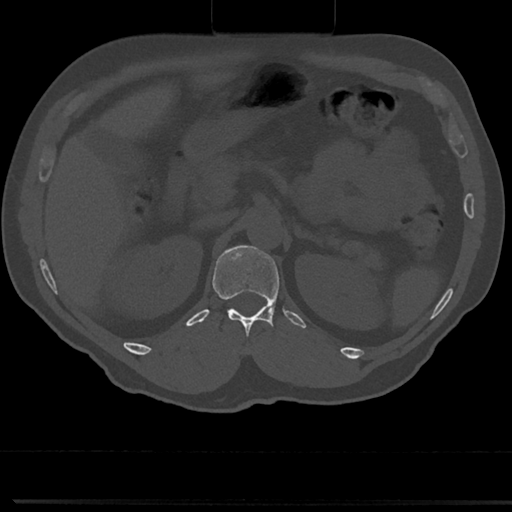
CT including the spine, one axial slice; slice 137 of 817 in the series (ordered by position); reconstruction kernel Br40s/3; bone window (W 1800 / L 400 HU); 0.5 mm slice thickness; 512 × 512 image matrix. Male patient, age 61 years. Case-level facts recorded for this patient, not image findings: primary cancer: prostate.
Annotated regions visible in this slice (semi-automatic segmentation, software-assisted and operator-edited):
- T12 vertebra: box from (x=213, y=260) to (x=282, y=357) px